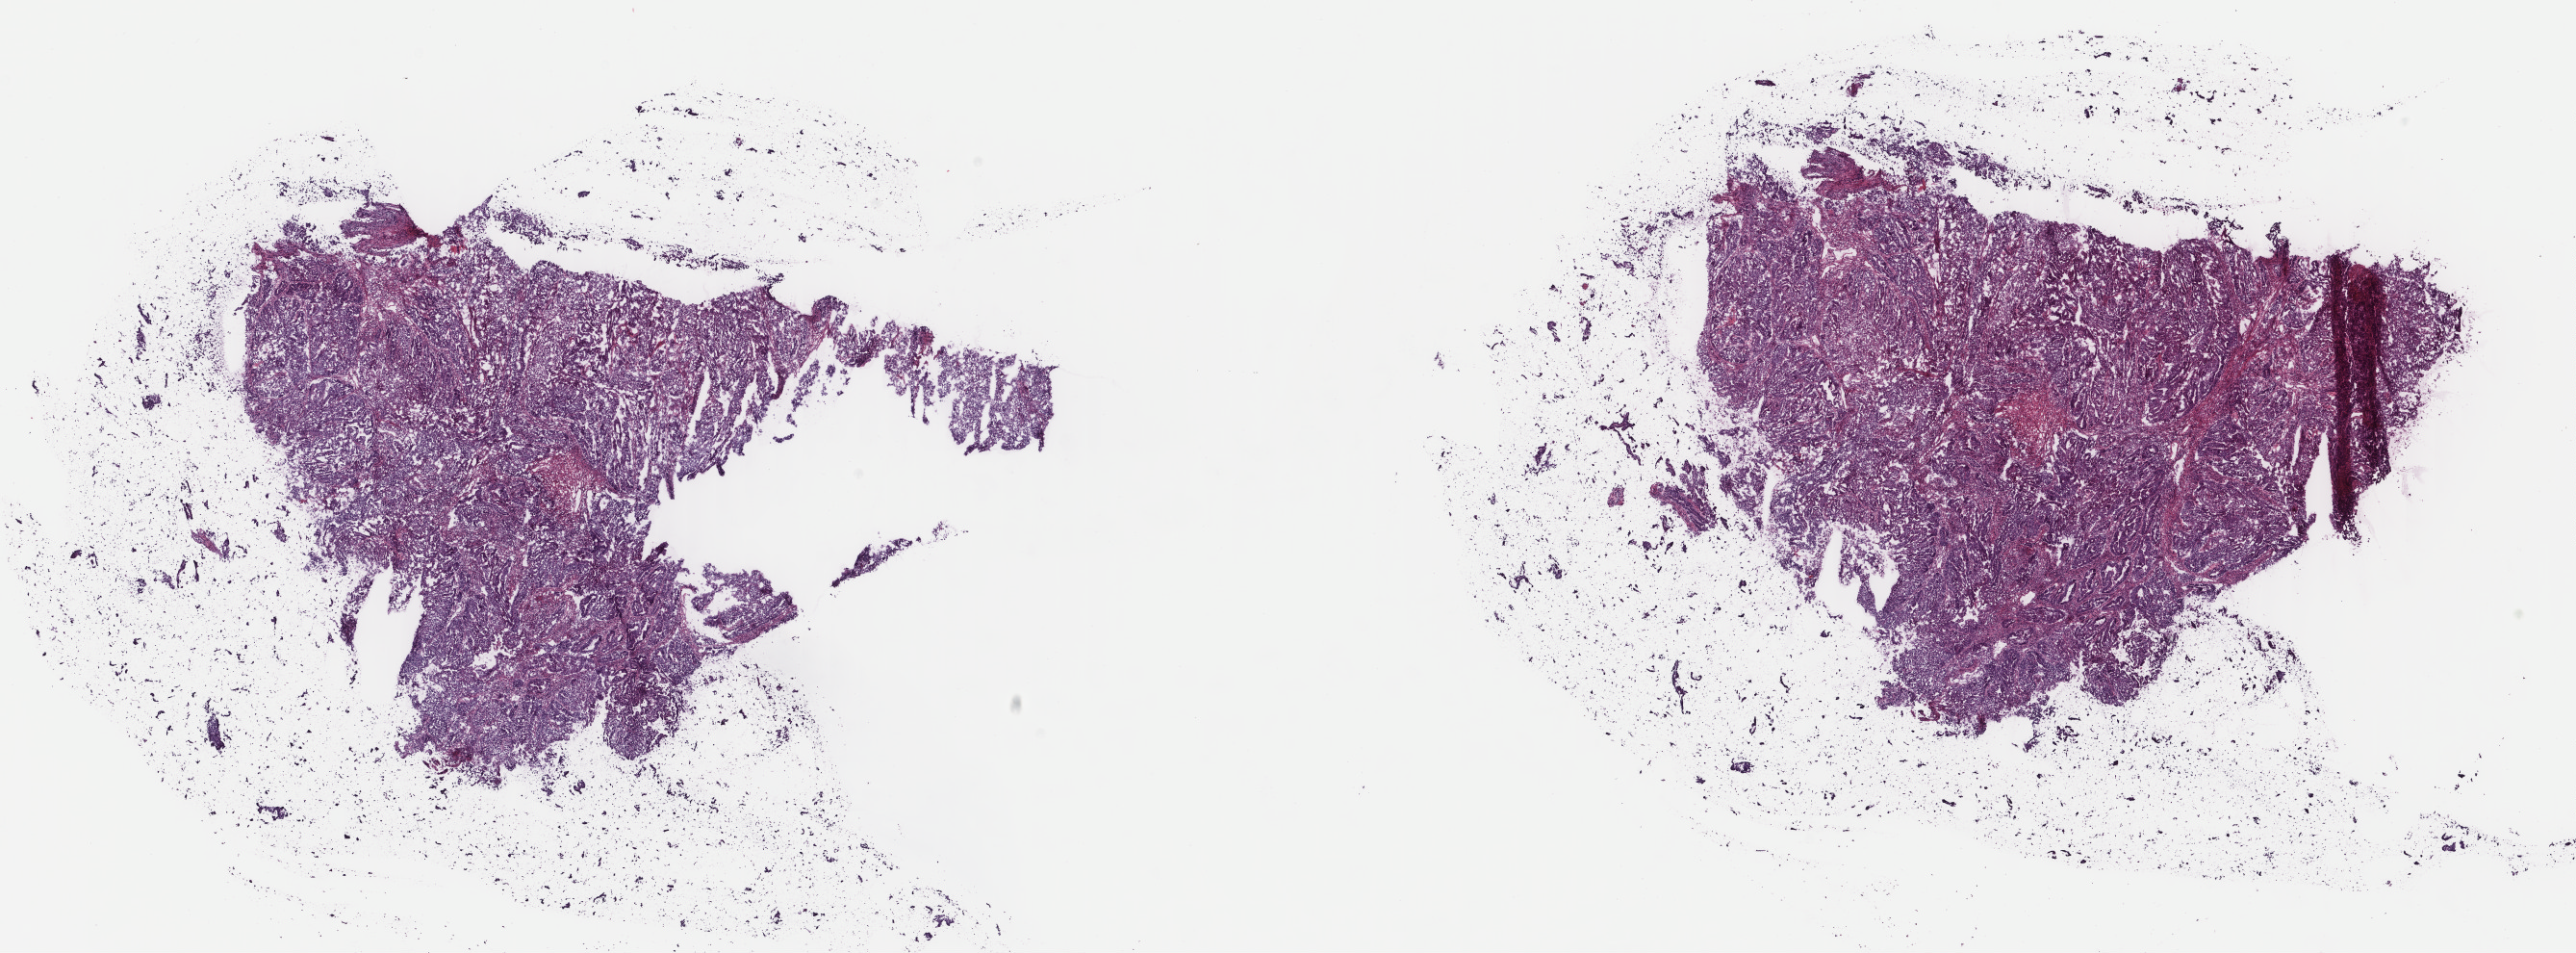
H&E whole-slide image — low-resolution overview of the scanned area, about 21.2 x 7.9 mm, frozen section from the top of the tissue portion, sample: primary tumour, uterus. Patient: female, age at initial diagnosis 56 years. Histologic grade: G3 (poorly differentiated). Composition of this section per pathologist review: tumour cells 70%, tumour nuclei 70%, normal cells 20%, stromal cells 9%, necrosis 1%. Infiltration values recorded for this section: lymphocyte infiltration 20%, monocyte infiltration 0%, neutrophil infiltration 0%.
Lymph nodes positive (case pathology): 0 of 2 examined. FIGO stage: IC. Diagnosis: Endometrioid adenocarcinoma, NOS (endometrium).